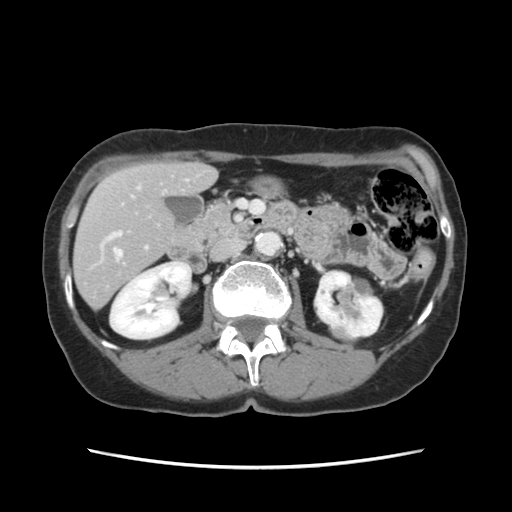
Contrast-enhanced abdominal CT, one axial slice. Slice 50 of 120 in the series (ordered by position). Soft-tissue window (W 400 / L 40 HU). 512 × 512 image matrix, field of view 330 × 330 mm. Female patient, age 70 years. Case-level facts recorded for this patient, not image findings: diagnosis: colorectal cancer liver metastases, imaged before liver resection; multiple liver metastases: no; largest metastasis: 2.5 cm; disease in both lobes: no.
Annotated regions visible in this slice (manually delineated by an expert):
- hepatic veins: bounding box [x1, y1, x2, y2] px = [114, 249, 122, 260]
- liver: [75, 163, 215, 308]
- planned liver remnant (the part of the liver to remain after resection): [75, 163, 215, 307]
- portal vein (with intrahepatic branches): [101, 180, 188, 249]